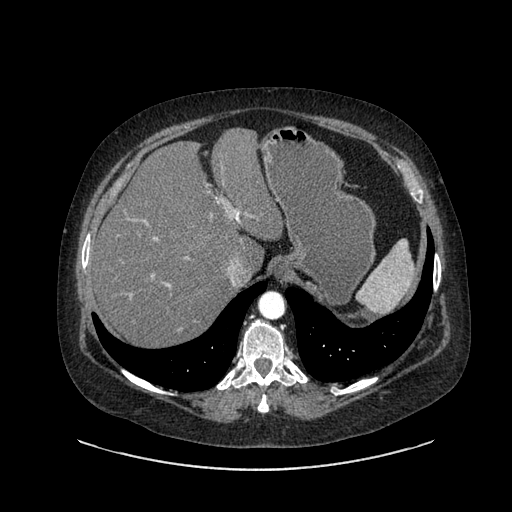
Contrast-enhanced abdominal CT, one axial slice; reconstruction kernel SOFT; intravenous contrast given; soft-tissue window (W 400 / L 40 HU); 0.62 mm slice thickness; 512 × 512 image matrix, field of view 460 × 460 mm. Patient: female, 61 years. From the clinical record (not read from this slice): diagnosis: adrenocortical carcinoma; tumour side: left adrenal; tumour size at pathology: 13 cm; Ki-67 index: 79 %; stage (as recorded): 2.
Outlined on this slice (semi-automatic segmentation, software-assisted and operator-edited):
- mass: bounding box [x1, y1, x2, y2] px = [345, 312, 360, 323]